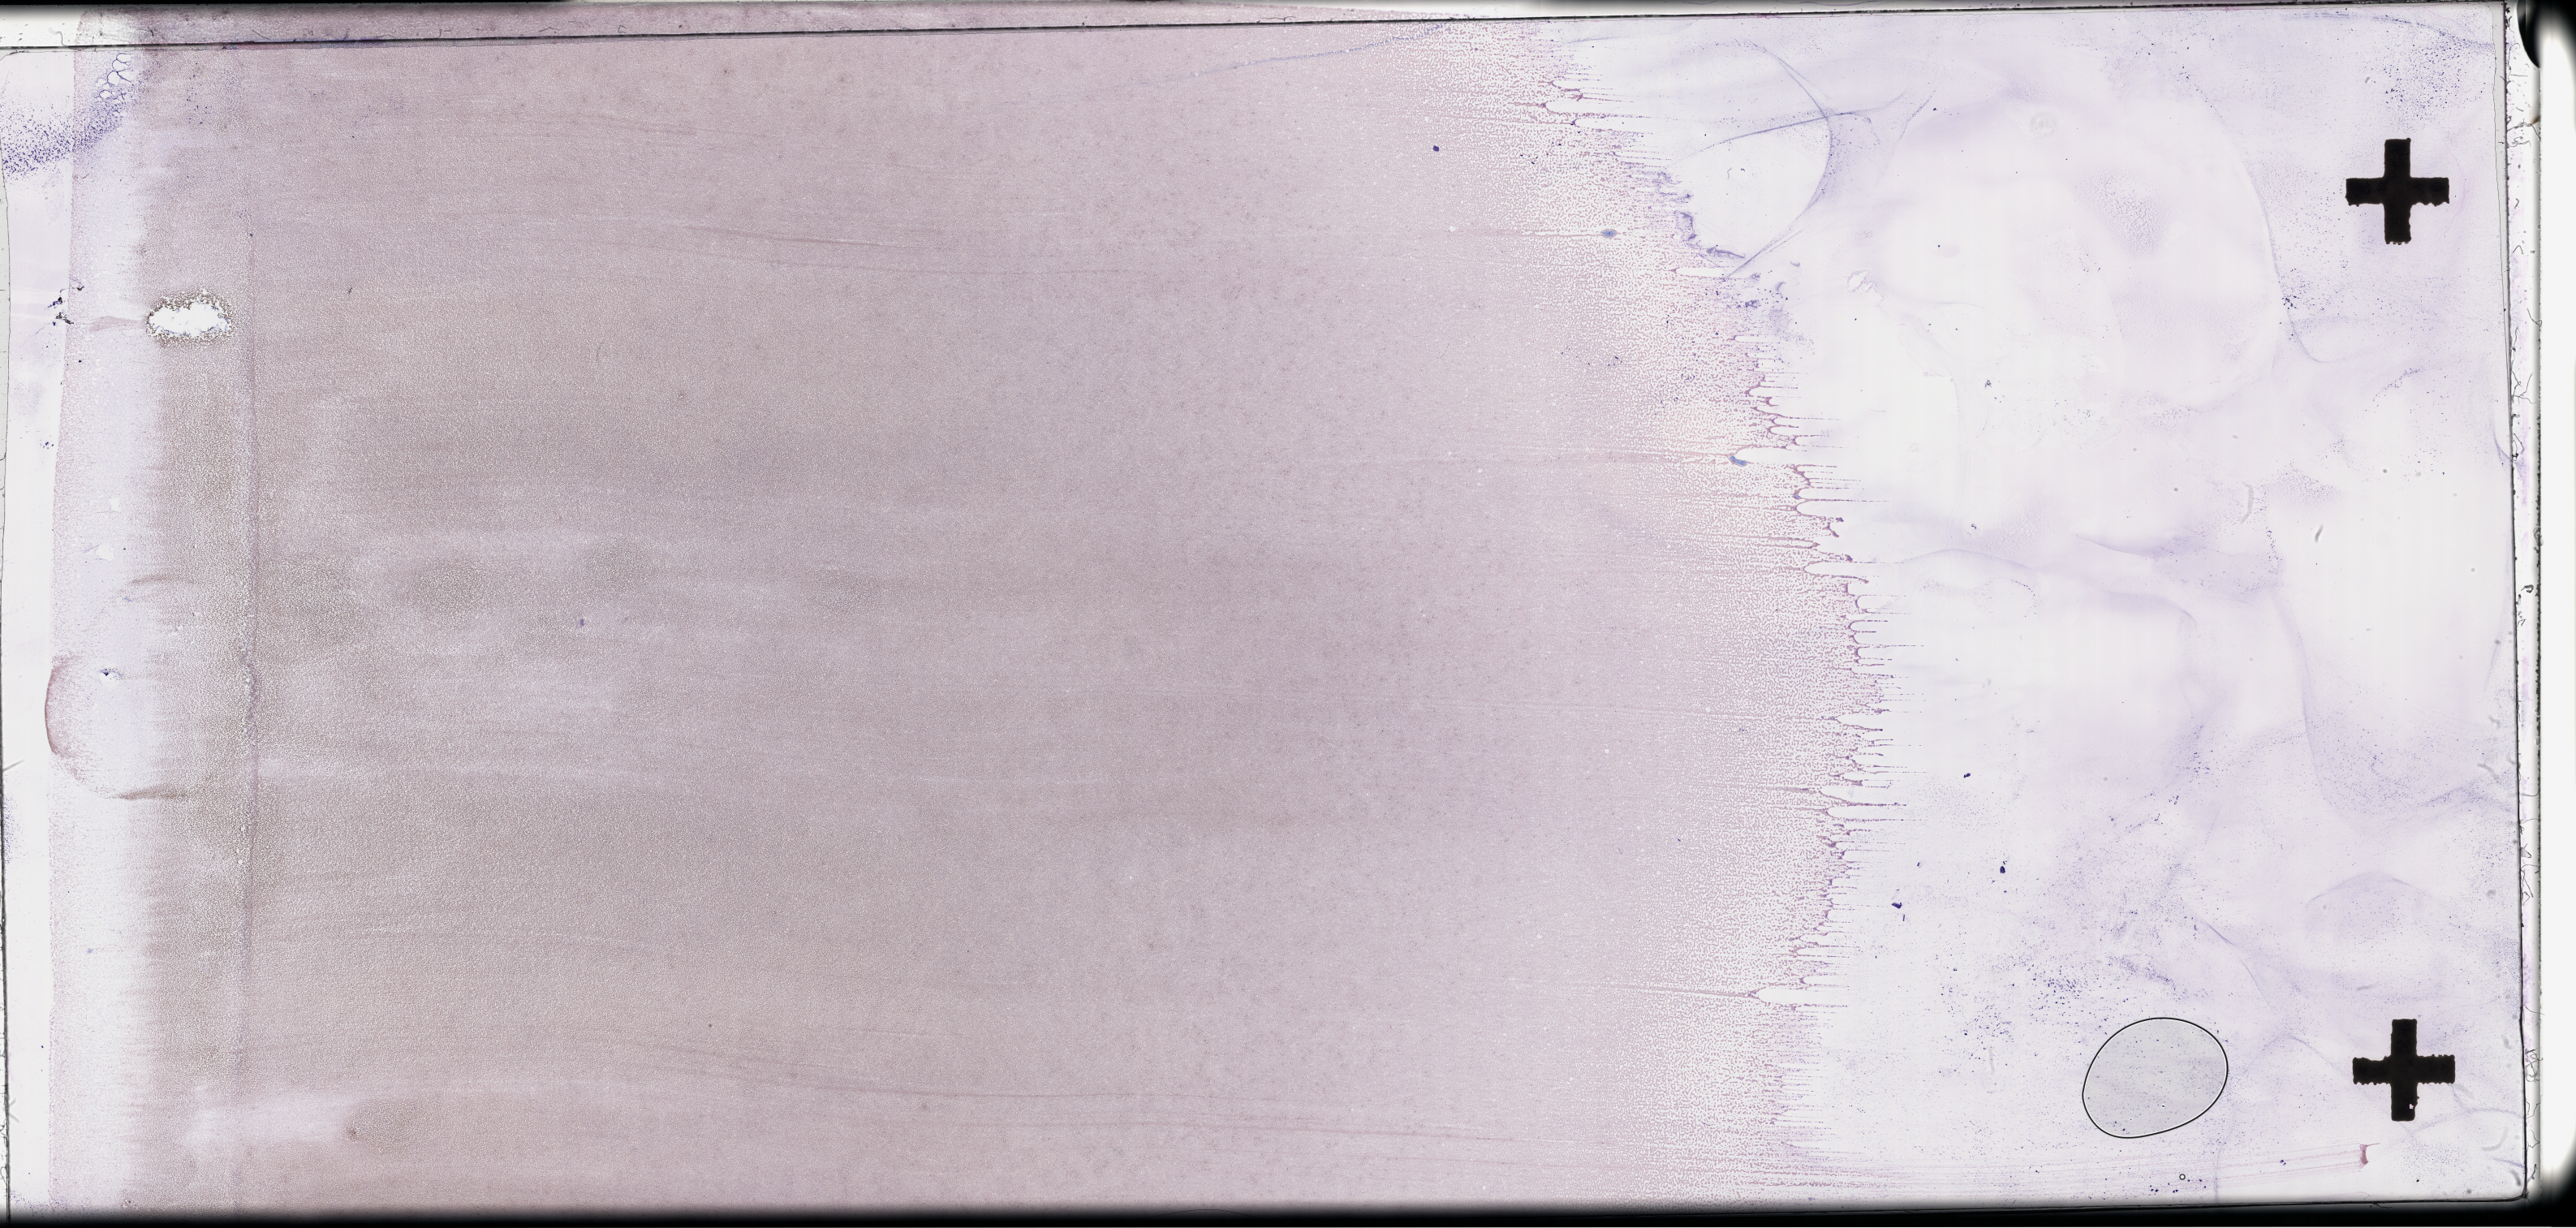
Whole-slide image of a whole blood smear, Wright-Giemsa stain — low-resolution overview of the scanned area, about 51.3 x 24.4 mm. Specimen time point: collected at disease progression. Female patient.
From a patient with: Plasma Cell Myeloma.